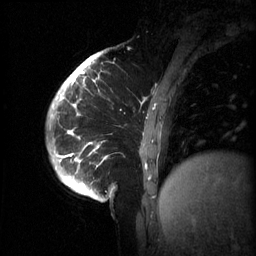
Breast MRI (dynamic contrast-enhanced), one sagittal slice; position 11 of 60 along the scan axis; 3 images stored at this slice position (order not interpretable as contrast timing); 1.5 T; TE 4.2 ms, TR 11 ms; 2 mm slice thickness; 256 × 256 image matrix, field of view 220 × 220 mm. Female patient, age 51 years.
Outlined on this slice (semi-automatic segmentation, software-assisted and operator-edited):
- analysis volume of interest (the breast-tissue region the enhancement analysis was run in; not a lesion): bounding box (x1, y1, x2, y2) in pixels: (63, 80, 187, 201)
- tumour enhancement mask (voxels above the 70 % enhancement threshold inside the analysis volume of interest): (63, 80, 155, 169)